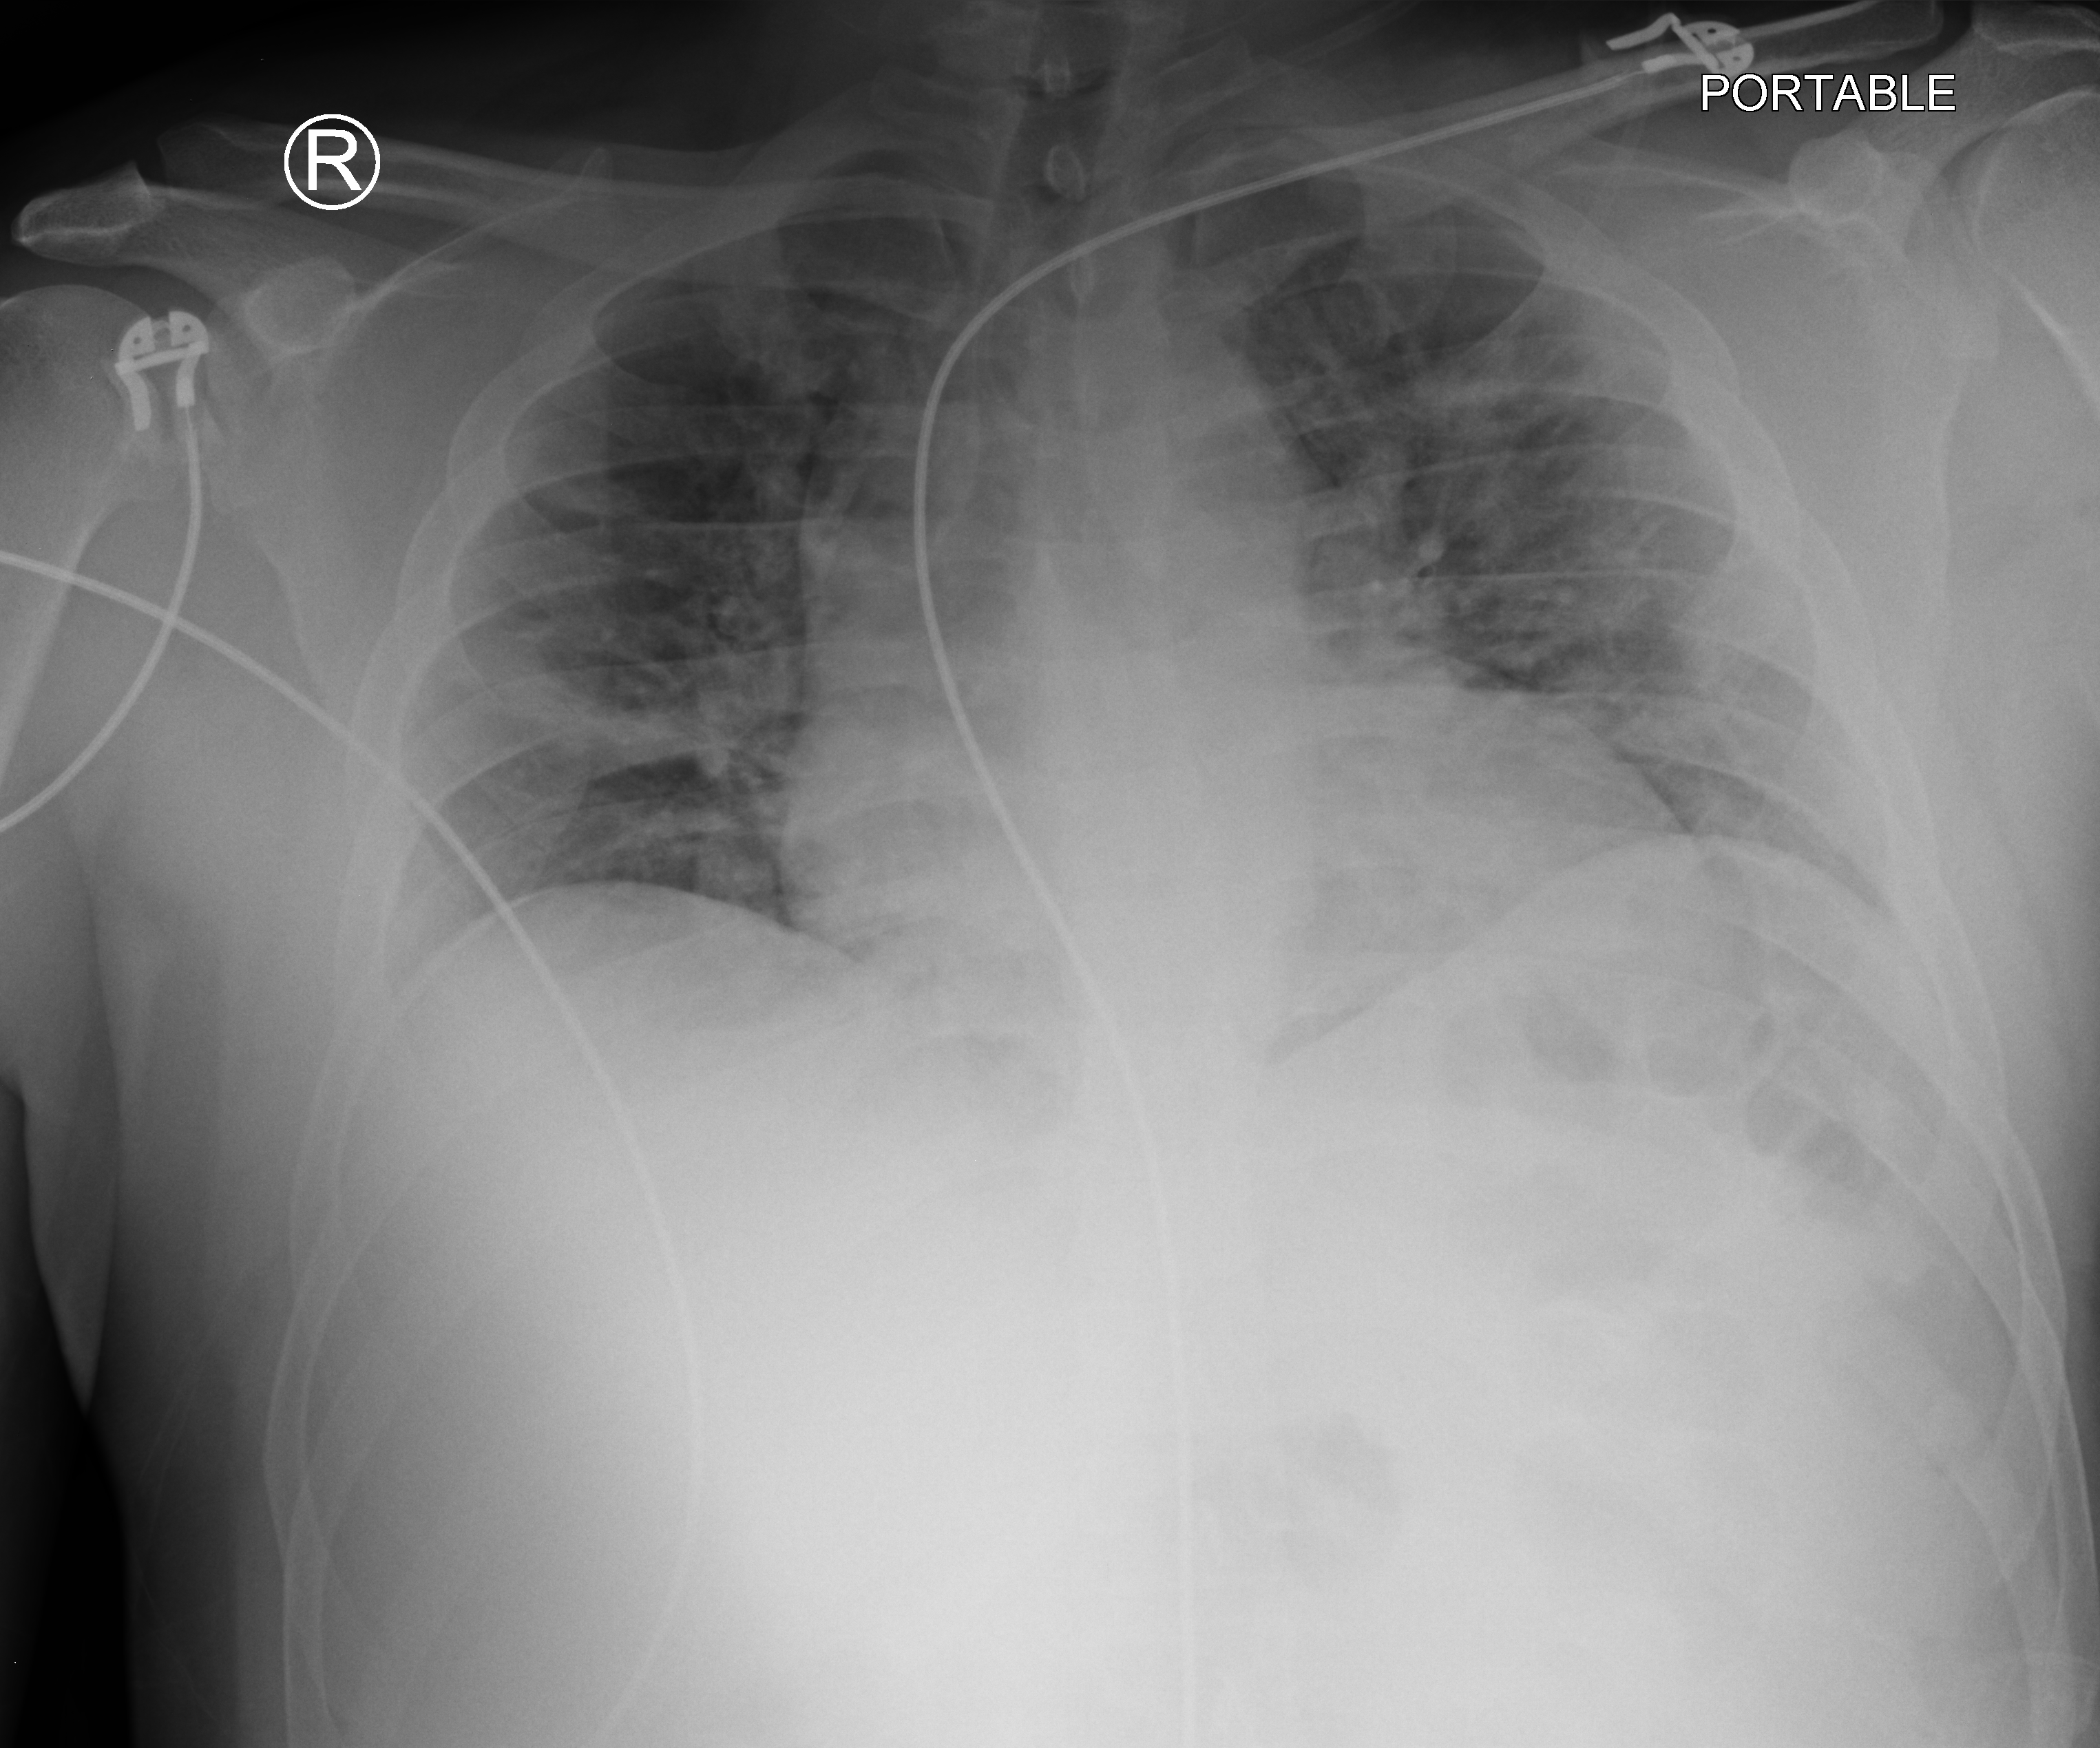
Chest X-ray (portable); anteroposterior (AP) projection. Patient hospitalised with COVID-19; male, aged 18–59 years.
From the hospital-stay record, not from the radiograph (when in the stay this image was taken is not recorded): admitted to intensive care during this hospital stay: no; mechanically ventilated during this hospital stay: no.